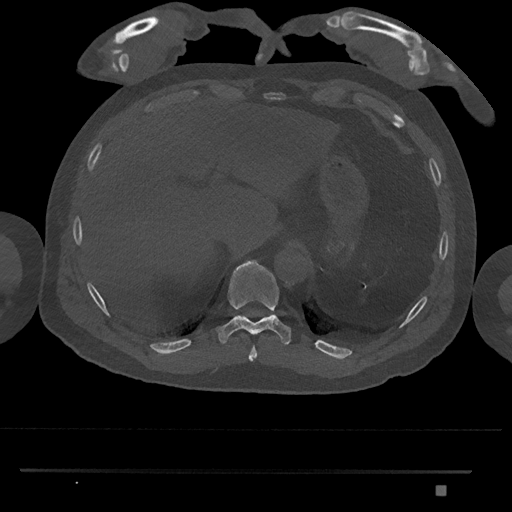
CT including the spine, one axial slice. Reconstruction kernel Br40s/3. 120 kVp. Bone window (W 1800 / L 400 HU). 0.5 mm slice thickness. 512 × 512 image matrix, field of view 429 × 429 mm. Male patient, age 65 years. From the clinical record (not read from this slice): primary cancer: prostate.
Outlined on this slice (semi-automatic segmentation, software-assisted and operator-edited):
- T10 vertebra: bounding box <216,260,291,346> (left, top, right, bottom; pixels)
- T9 vertebra: <248,346,257,362>